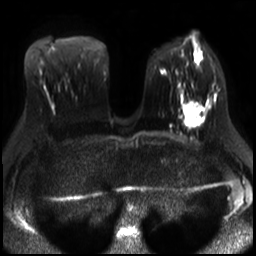
Breast MRI, one axial slice. Slice 13 of 30 in the series (ordered by position). Diffusion-weighted series; image 2 of 4 stored at this slice position (different b-values; order by instance number). 3 T. 4 mm slice thickness. 256 × 256 image matrix, field of view 320 × 320 mm. Female patient.
Annotated regions visible in this slice (expert manual segmentation):
- tumour on diffusion-weighted imaging: bounding box [x1, y1, x2, y2] px = [184, 102, 203, 120]